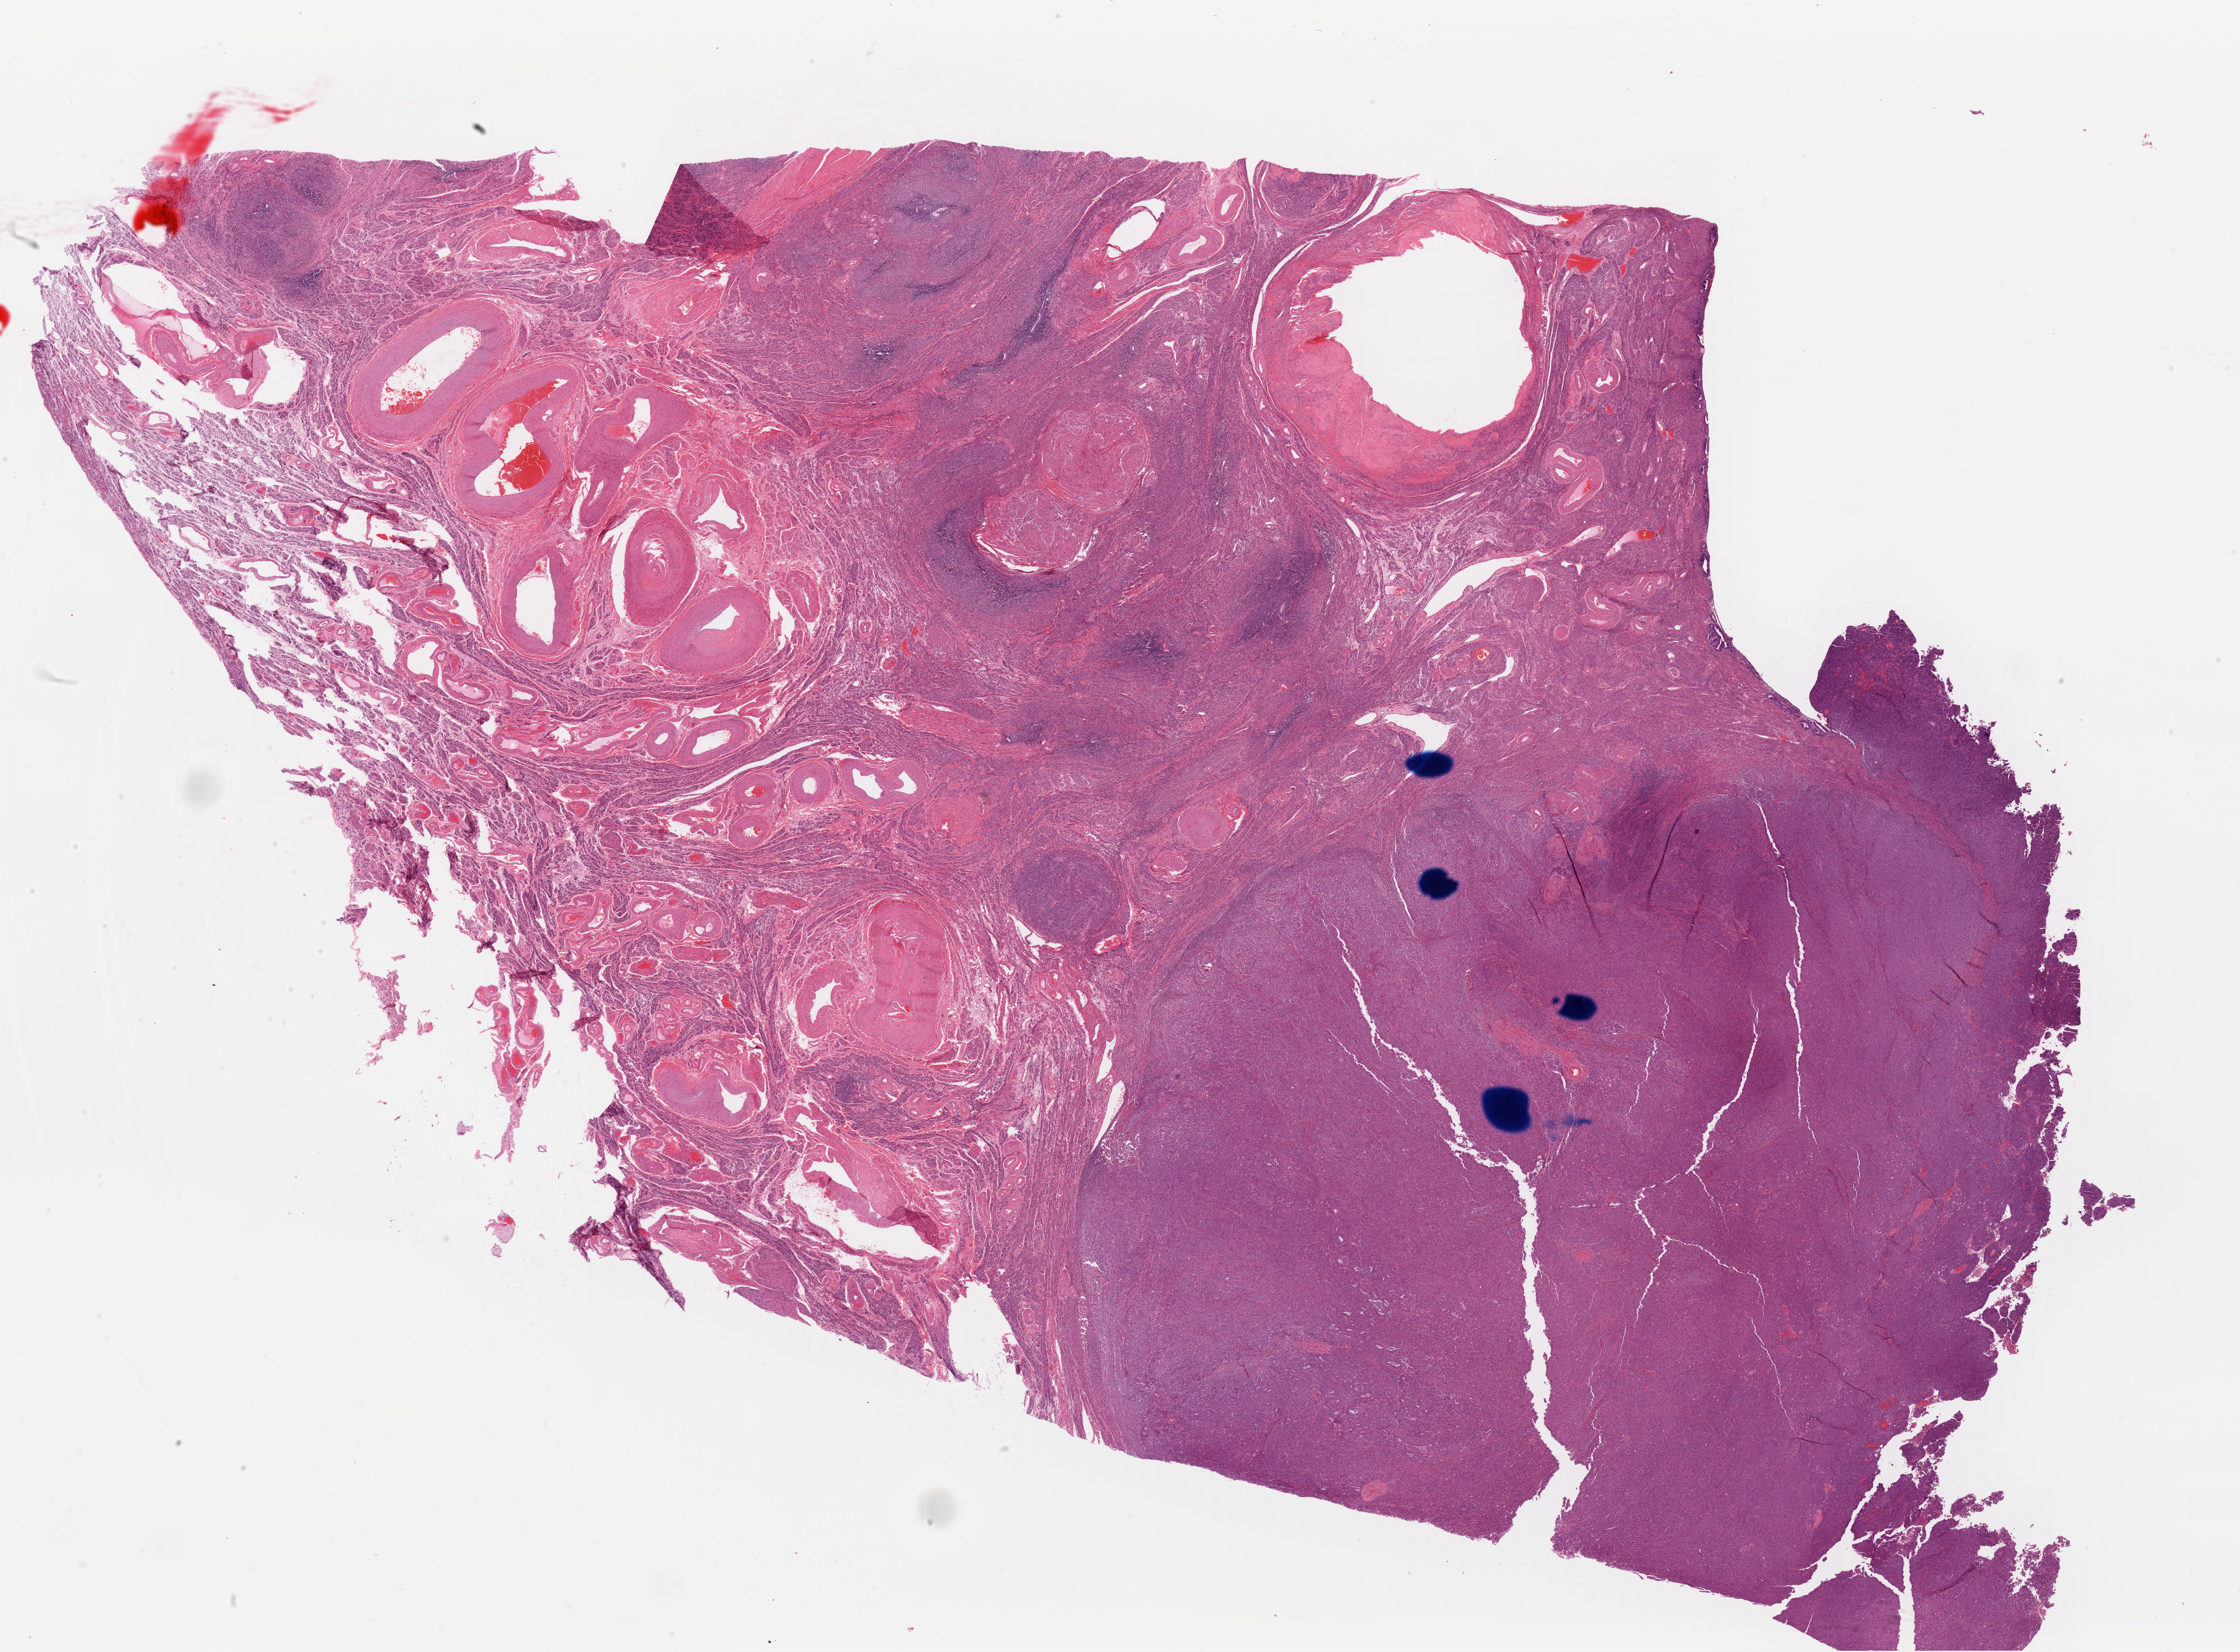
Digitized Hematoxylin and eosin (H&E) stained tissue section (whole slide), shown as a low-resolution overview of the whole scanned area (about 29.6 x 21.8 mm); formalin-fixed paraffin-embedded (FFPE) diagnostic section; sample: primary tumour, uterus. Female patient; age at initial diagnosis 64 years. Histologic grade: G3 (poorly differentiated).
FIGO stage: IC. Diagnosis: Endometrioid adenocarcinoma, NOS (endometrium). Lymph nodes positive (case pathology): 0 of 28 examined.